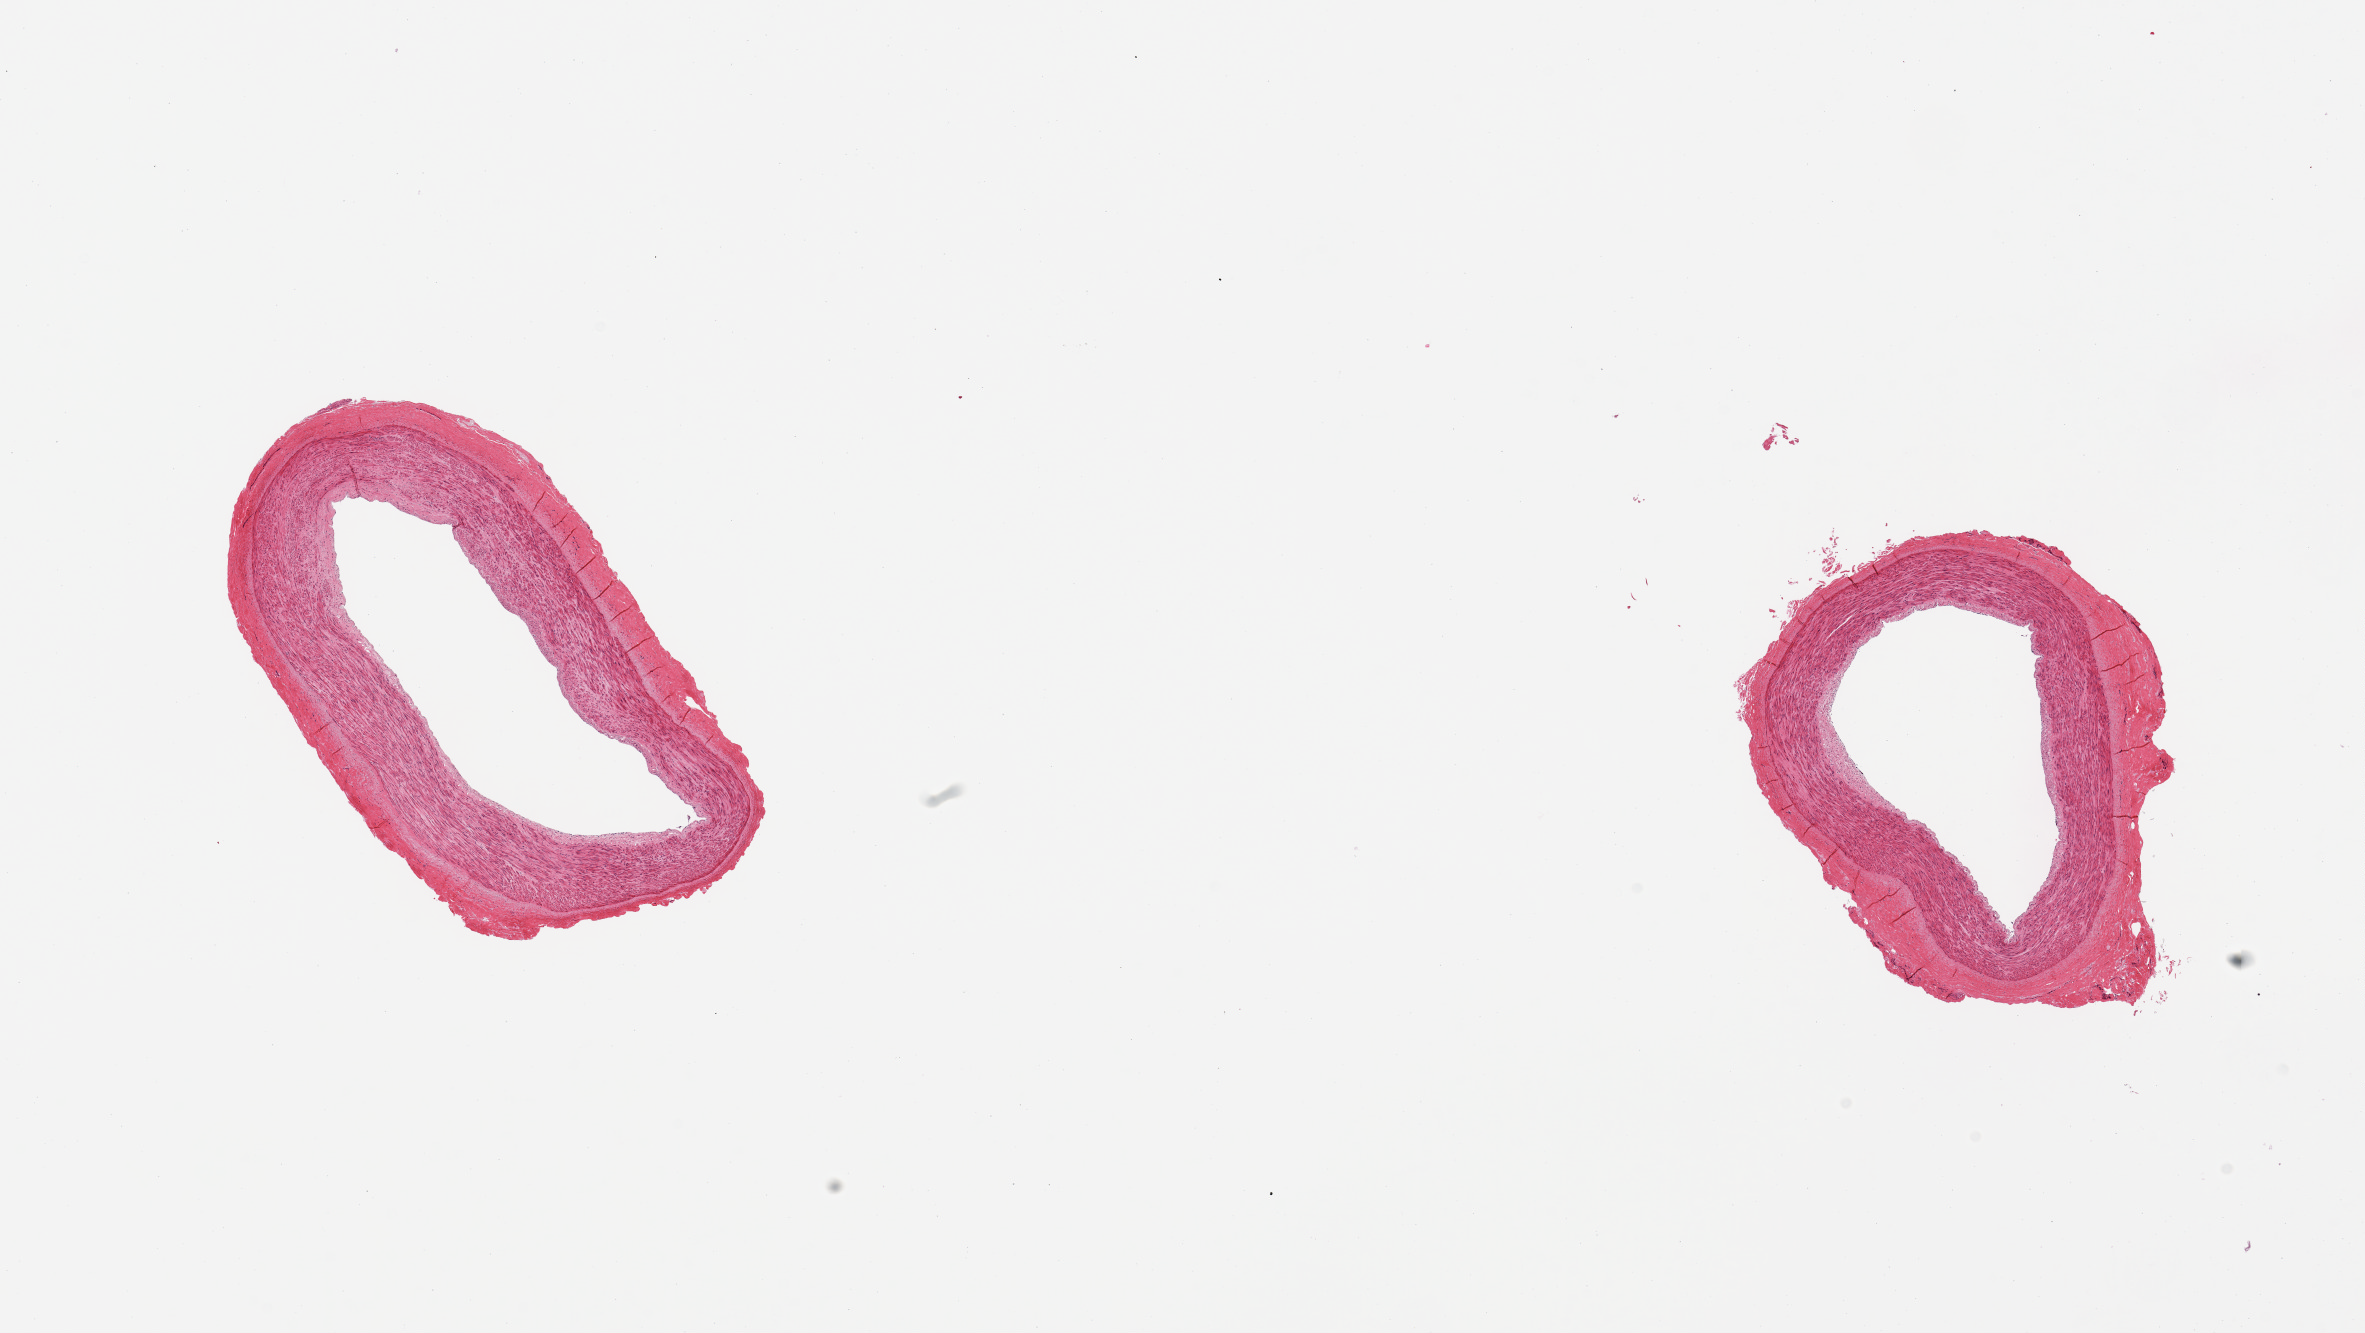
Digitized hematoxylin and eosin (H&E)-stained section, whole scanned area (about 18.7 x 10.5 mm) shown as a low-resolution overview. PAXgene-fixed, paraffin-embedded tissue. Target tissue: tibial artery. Tissue donor sample.
- pathologist's review note for this sample: 2 pieces; focal intimal thickening